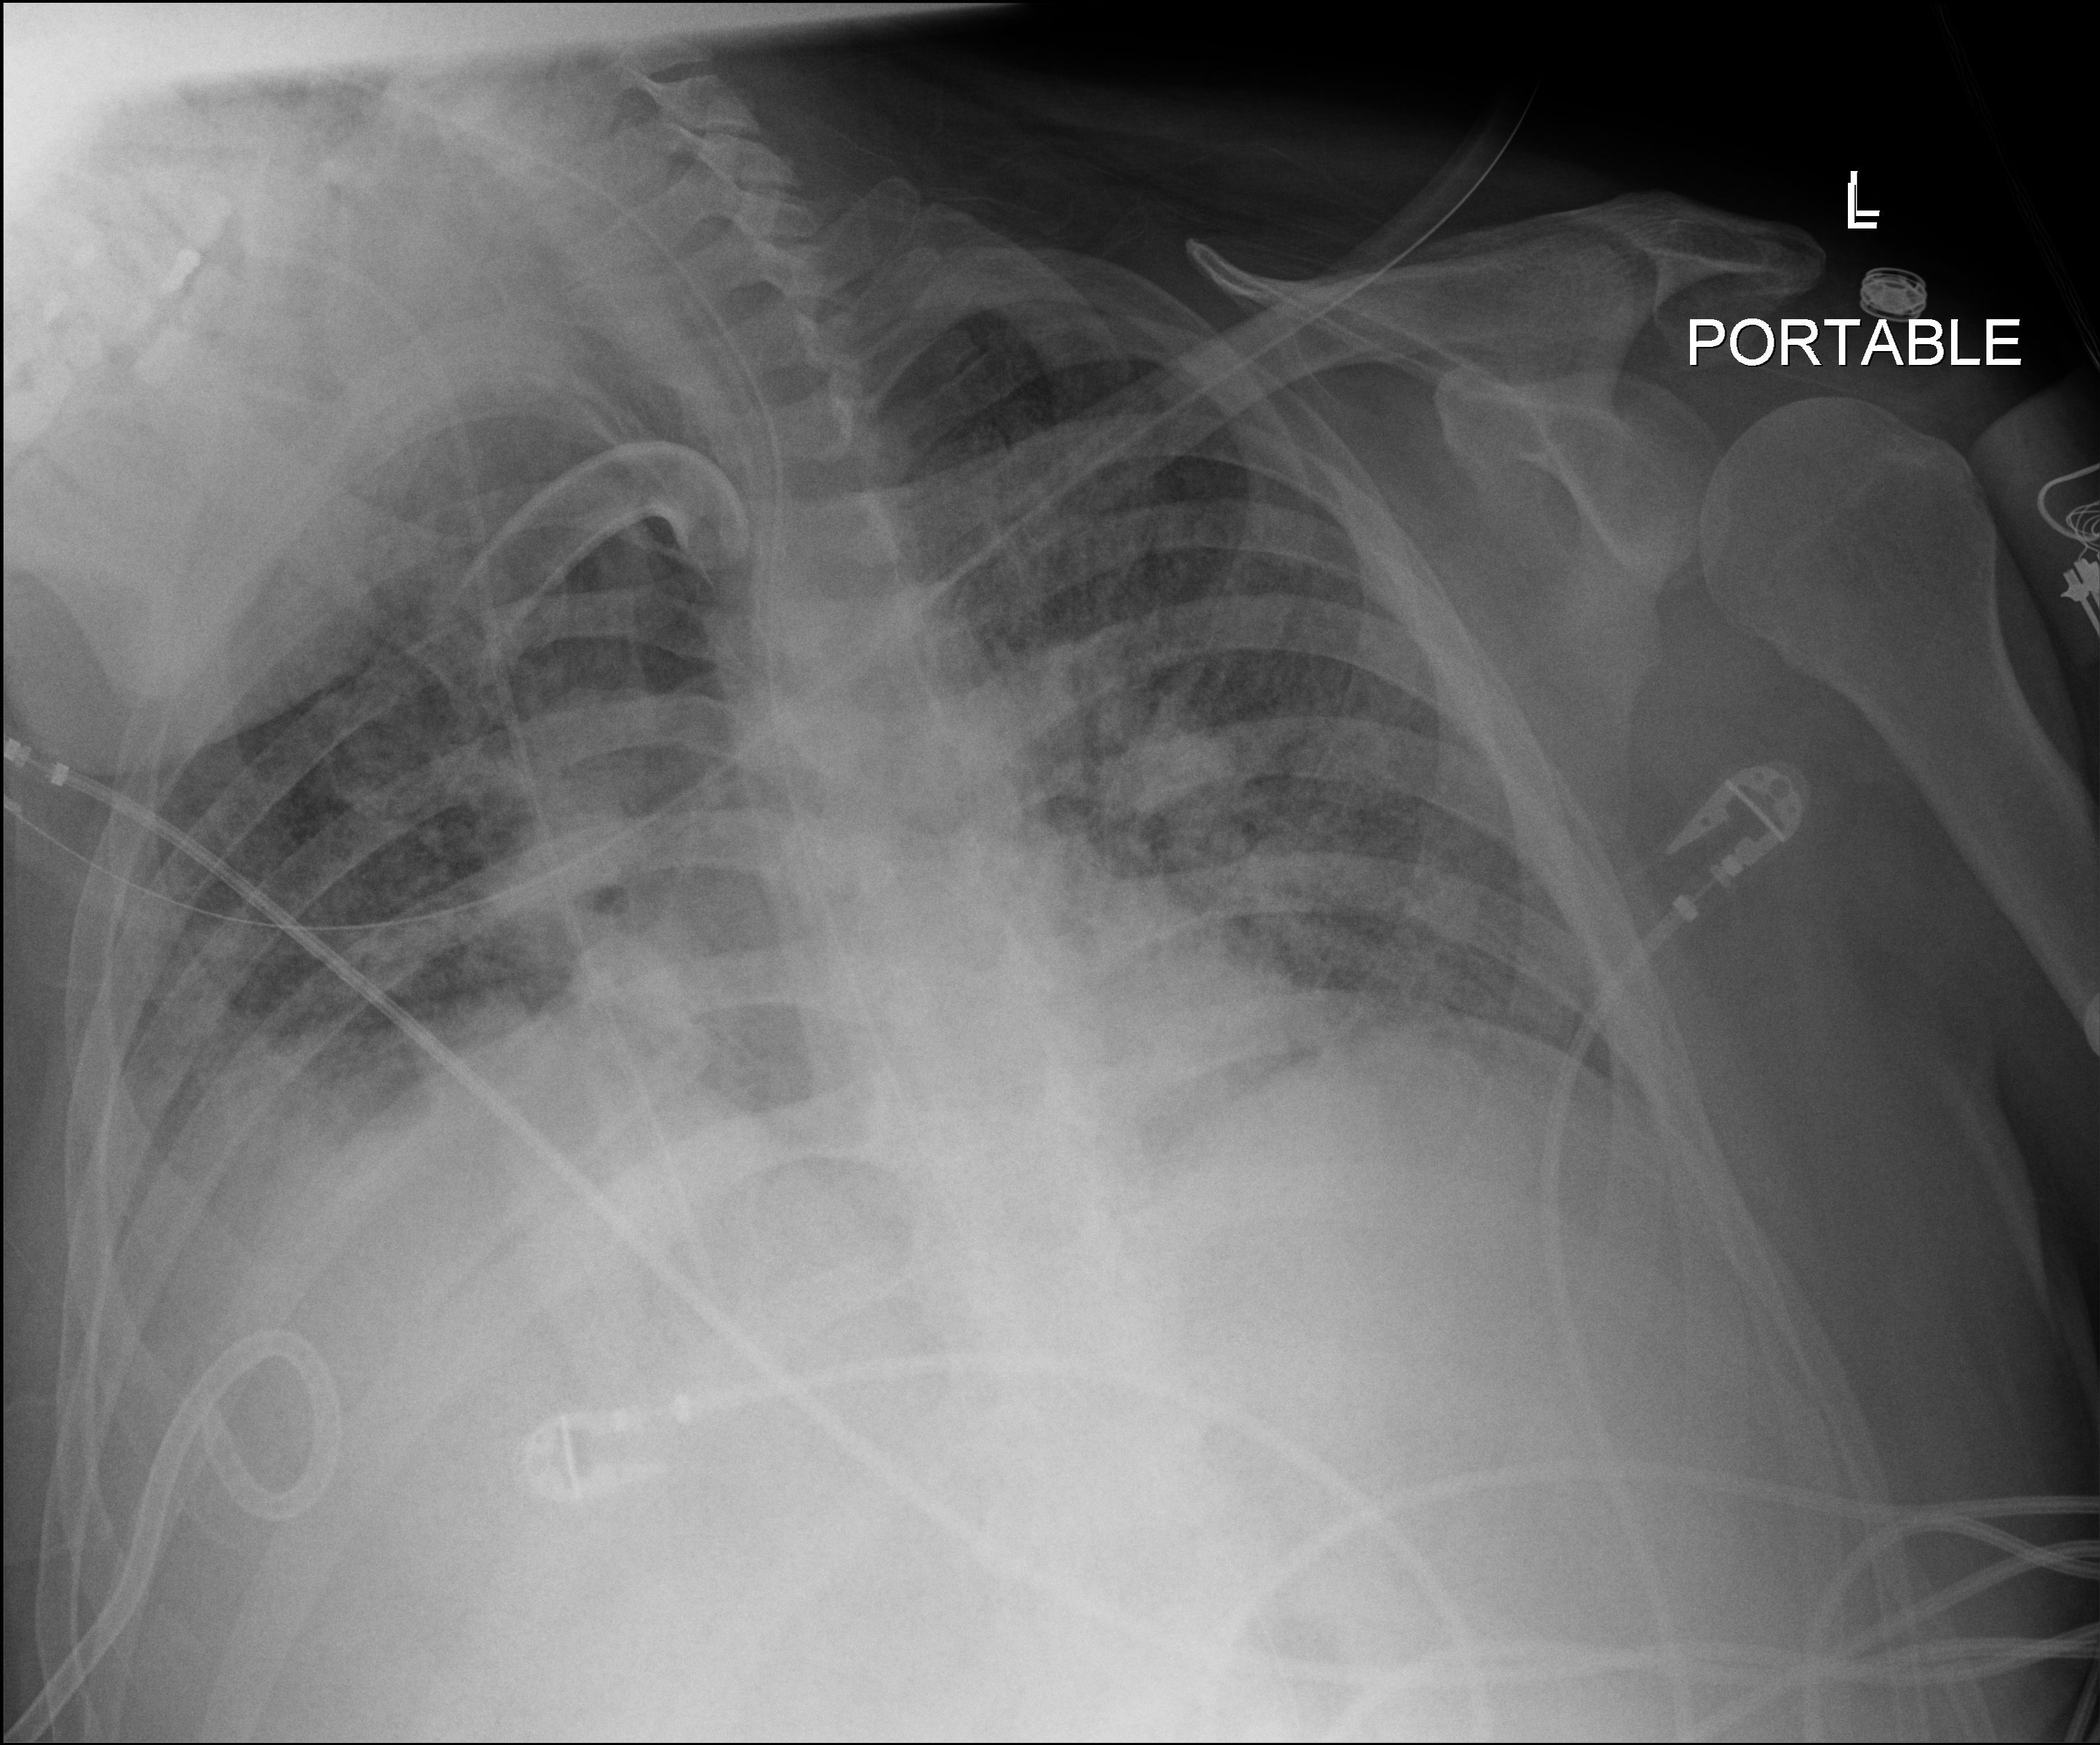
Chest X-ray (portable); anteroposterior (AP) projection. Patient hospitalised with COVID-19; male, aged 18–59 years.
From the hospital-stay record, not from the radiograph (when in the stay this image was taken is not recorded): hypertension (admission record): yes; smoking status (admission record): never.